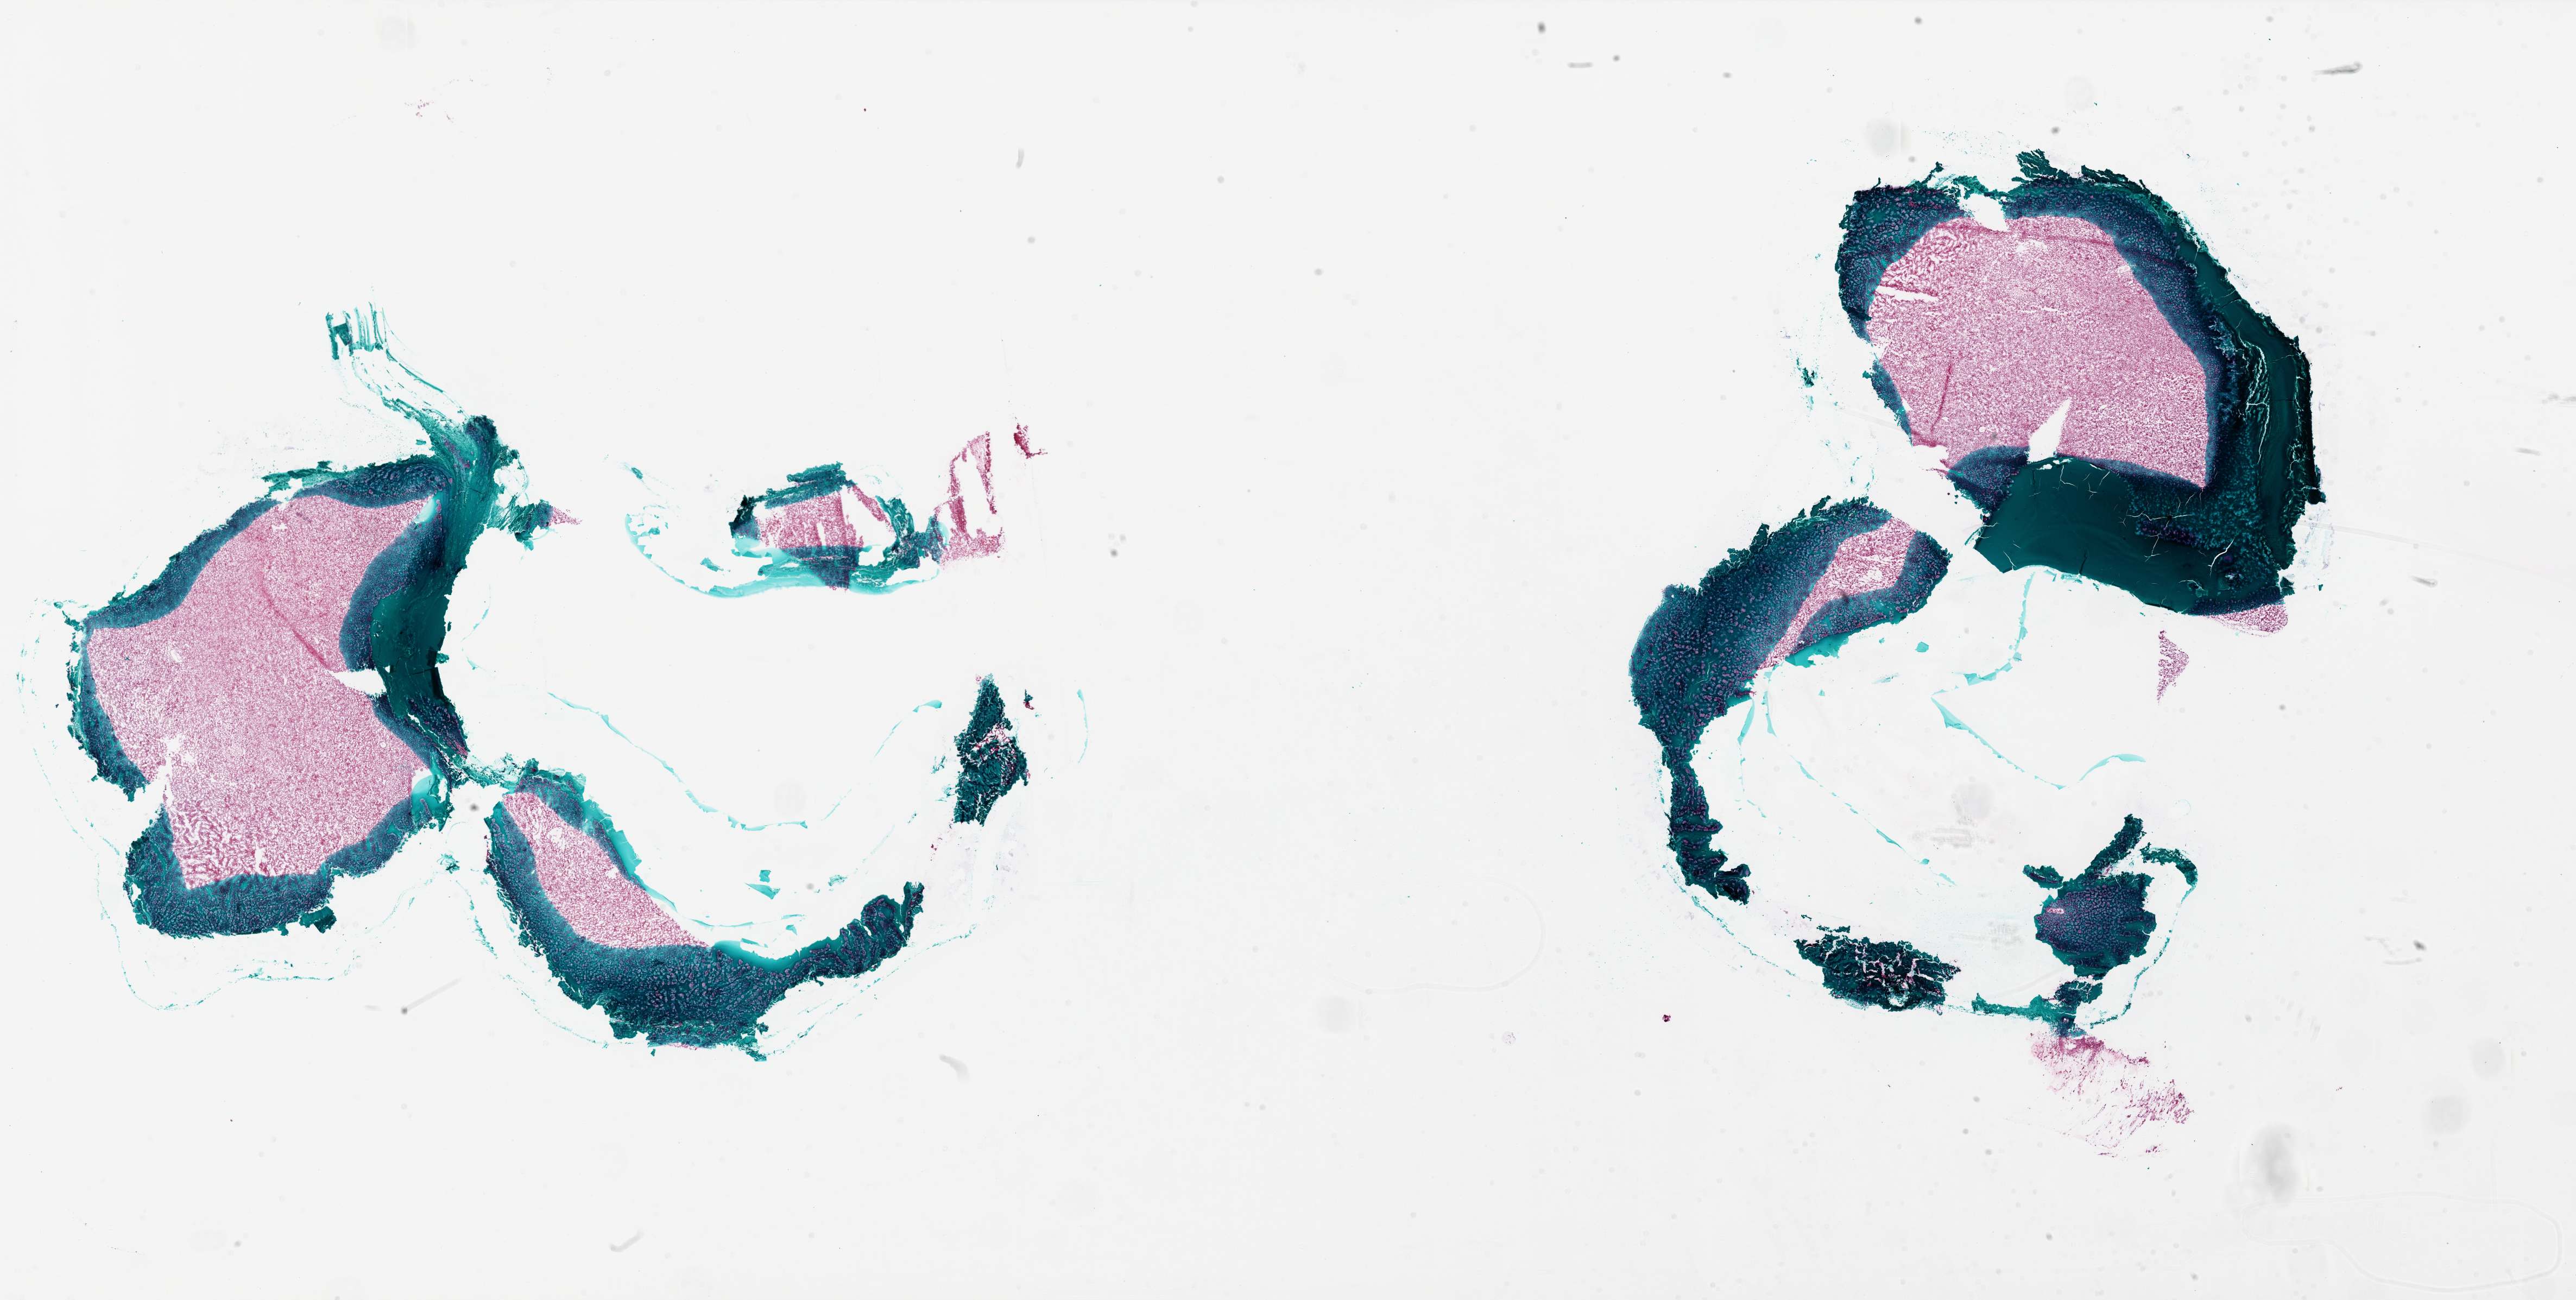
Whole-slide histology image, H&E-stained — shown as a low-resolution overview of the whole scanned area (about 38.0 x 19.2 mm, acquisition: 20x scan), frozen section from the bottom of the tissue portion, sample: primary tumour, brain. Patient: female, age at initial diagnosis 44 years. Slide review estimates, as recorded: tumour cells 100%, tumour nuclei 95%, normal cells 0%, stromal cells 0%, necrosis 0%. Infiltration values recorded for this section: lymphocyte infiltration 100%.
Pathologic diagnosis: Glioblastoma.